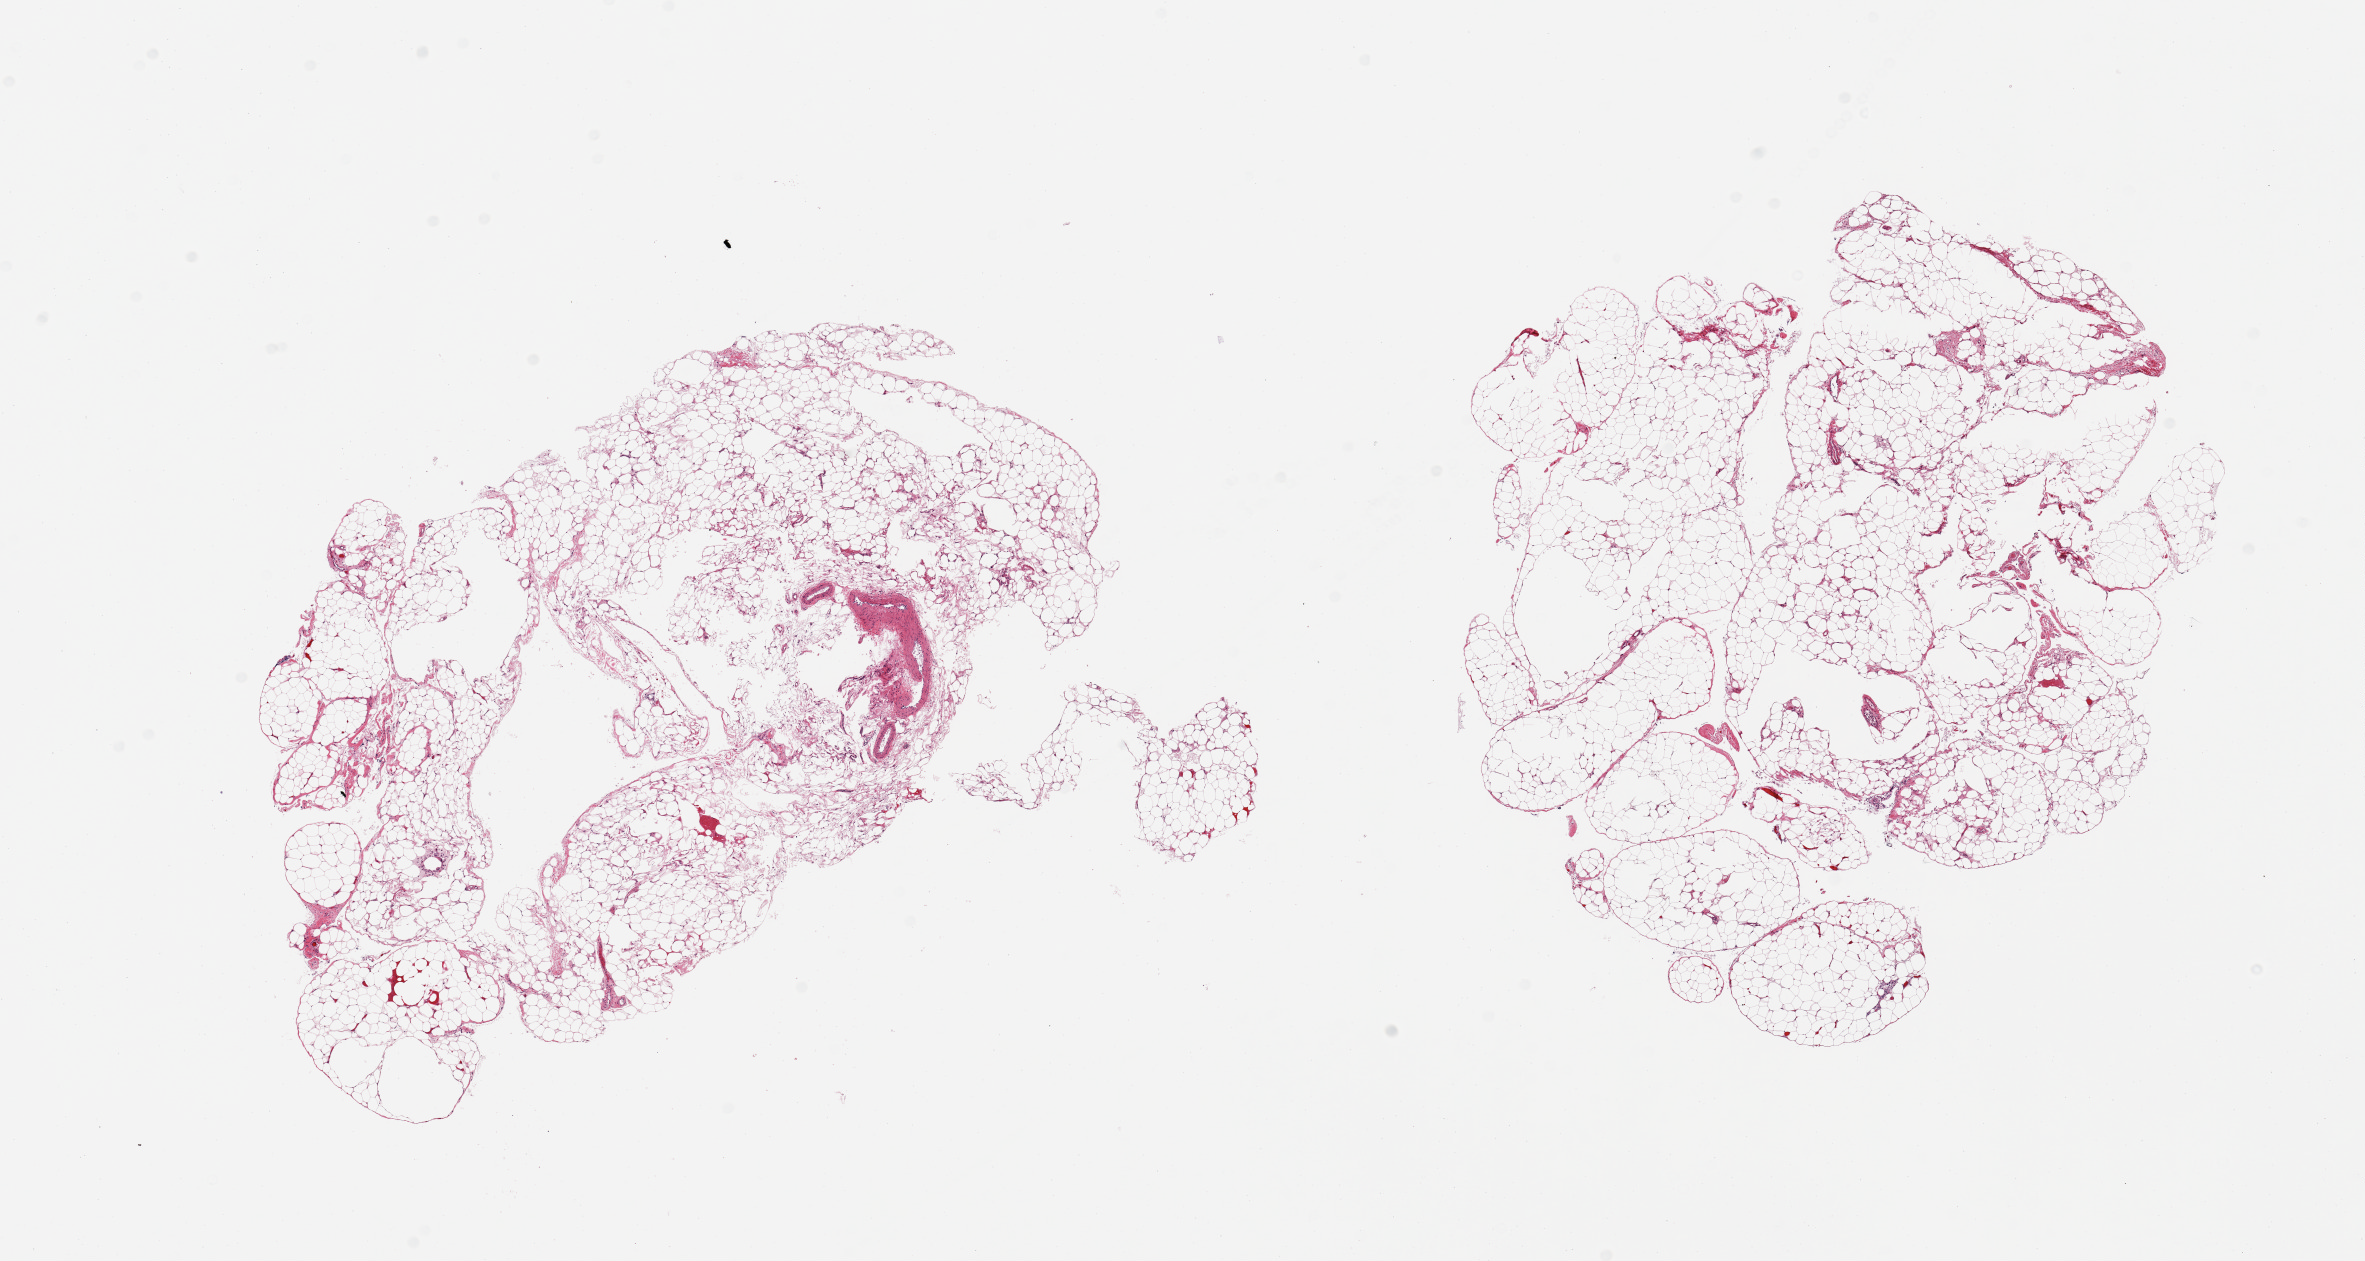
Whole-slide image, haematoxylin and eosin stain, whole scanned area (about 18.7 x 10.0 mm) shown as a low-resolution overview, PAXgene-fixed, paraffin-embedded tissue, sampled site (target tissue): omentum, tissue donor sample. Donor sex: male.
* pathologist's review note for this sample: 2 pieces; lobulated mature adipose tissue and minimal fibrovascular component